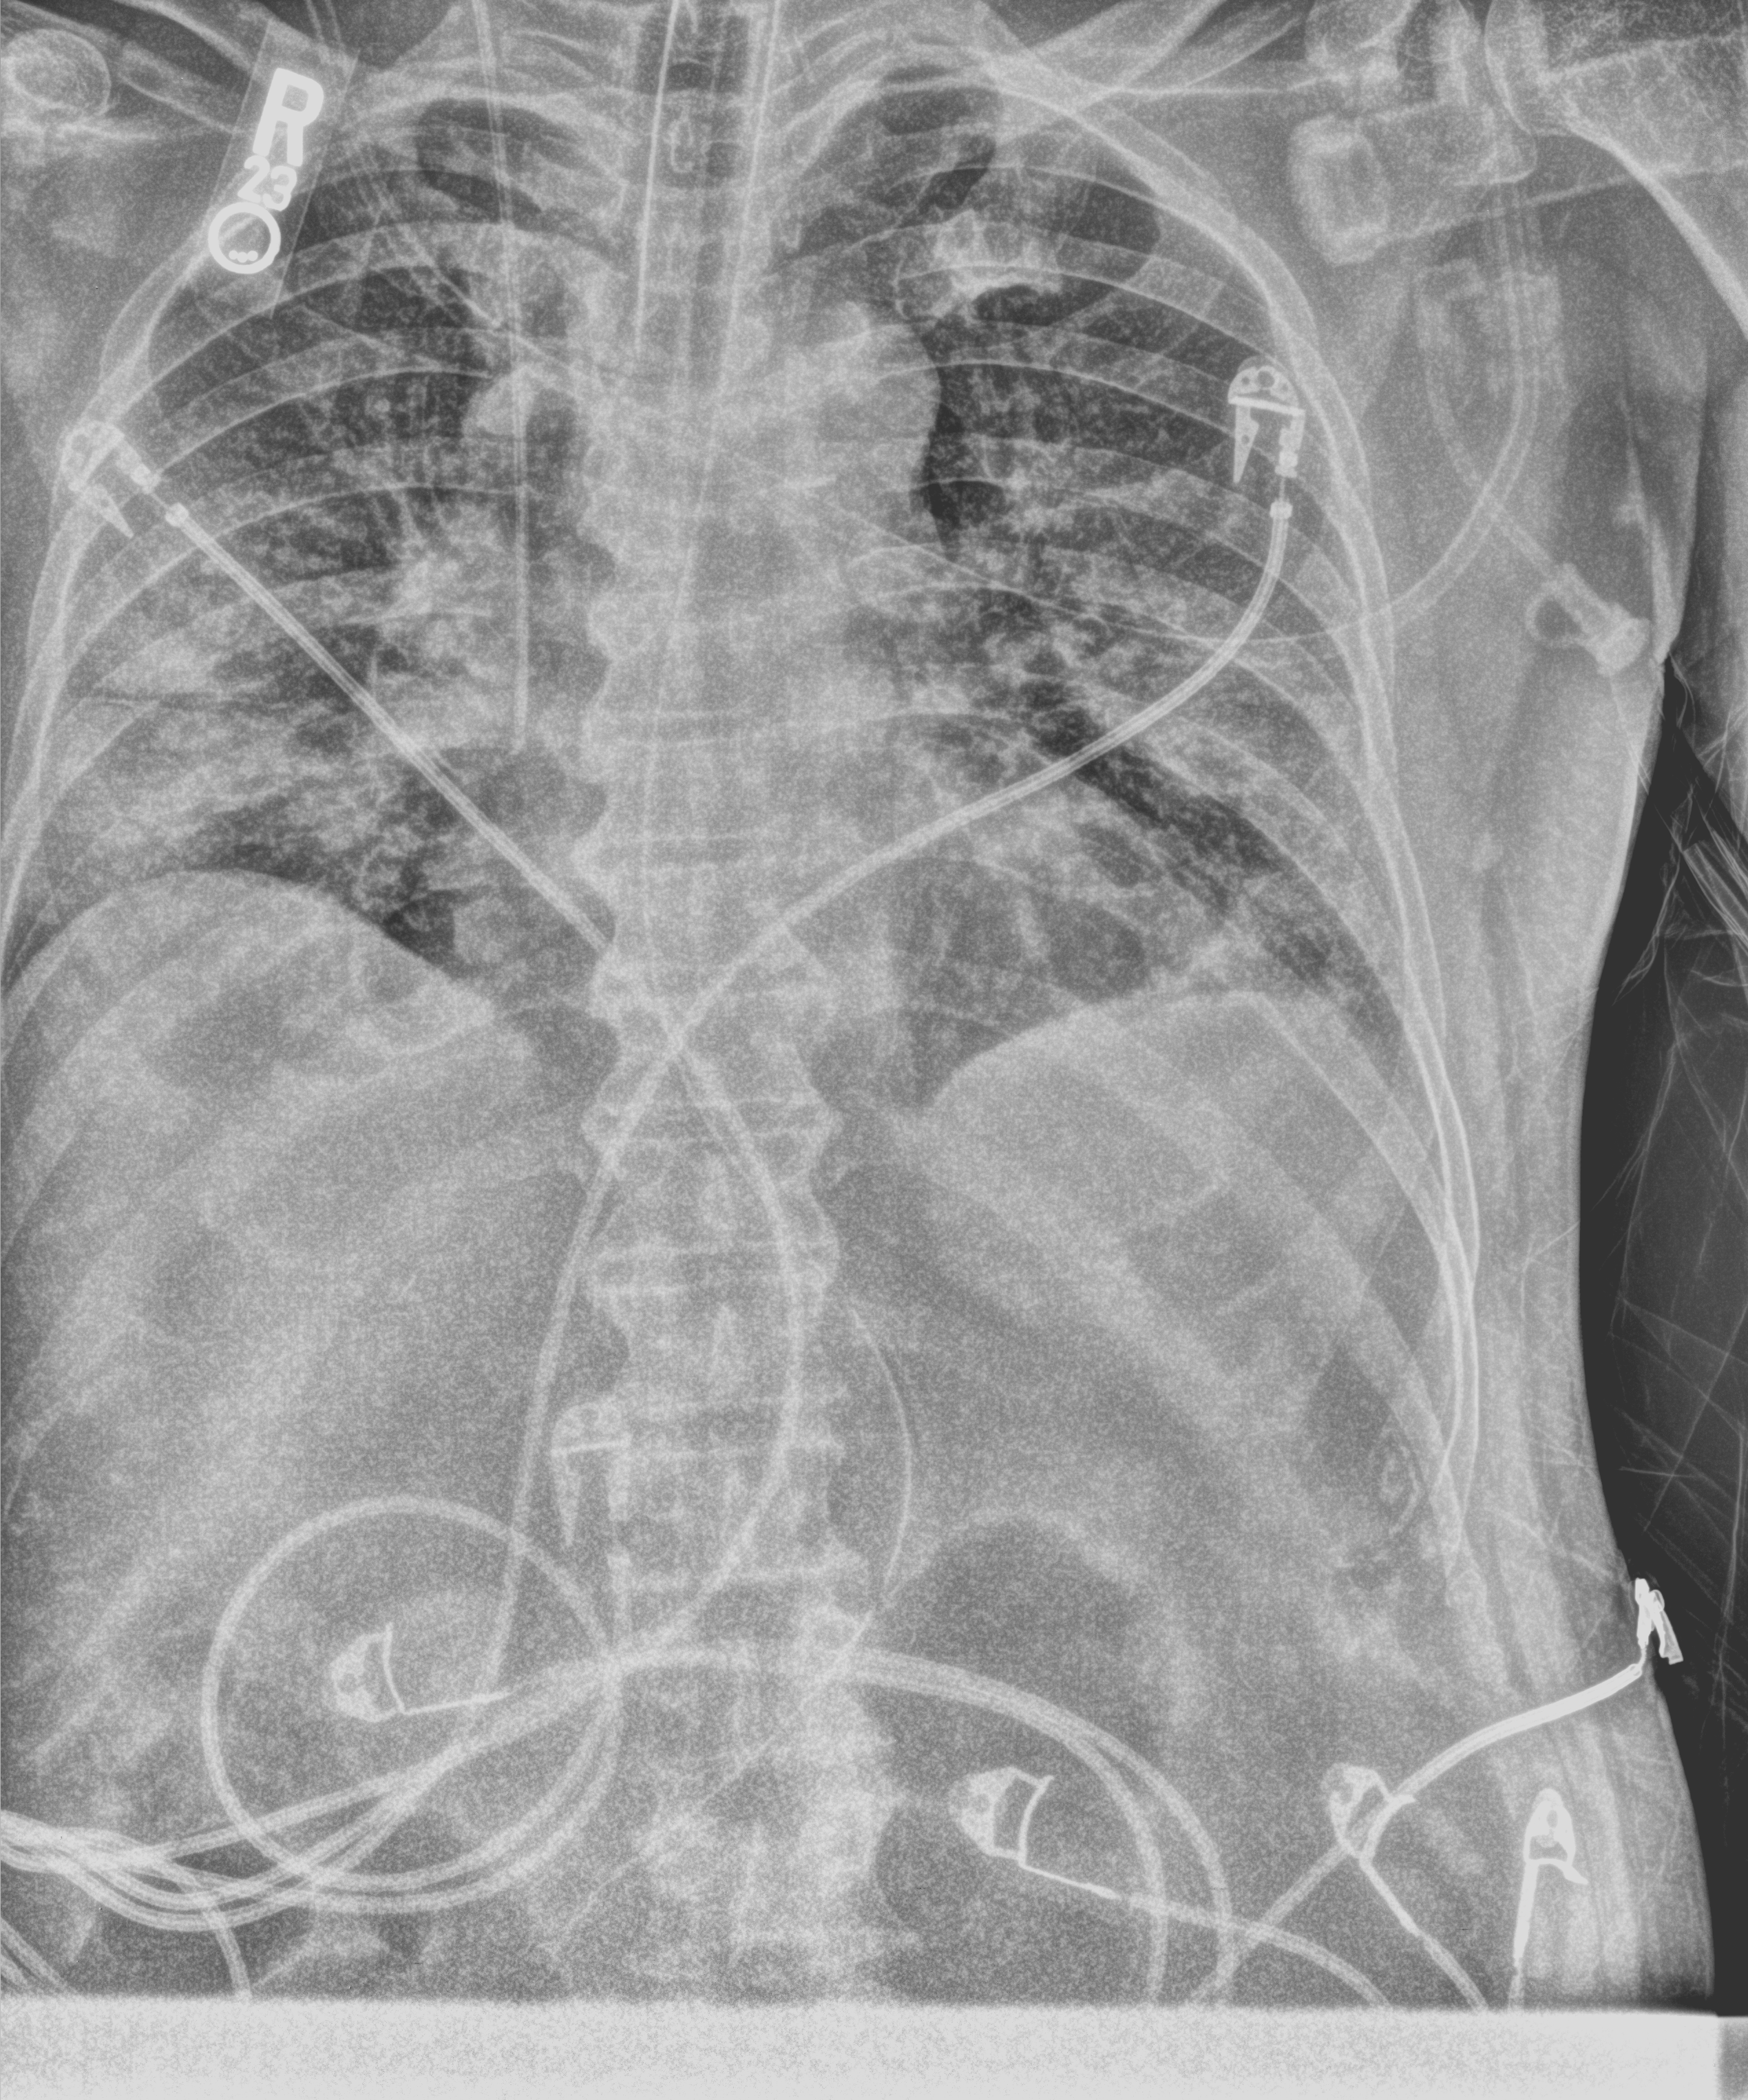
Chest X-ray (portable). Male patient hospitalised with COVID-19, age 60–74 years.
Admission-level facts for this patient (not findings on this image; timing relative to this image not recorded):
- other chronic lung disease (admission record): no